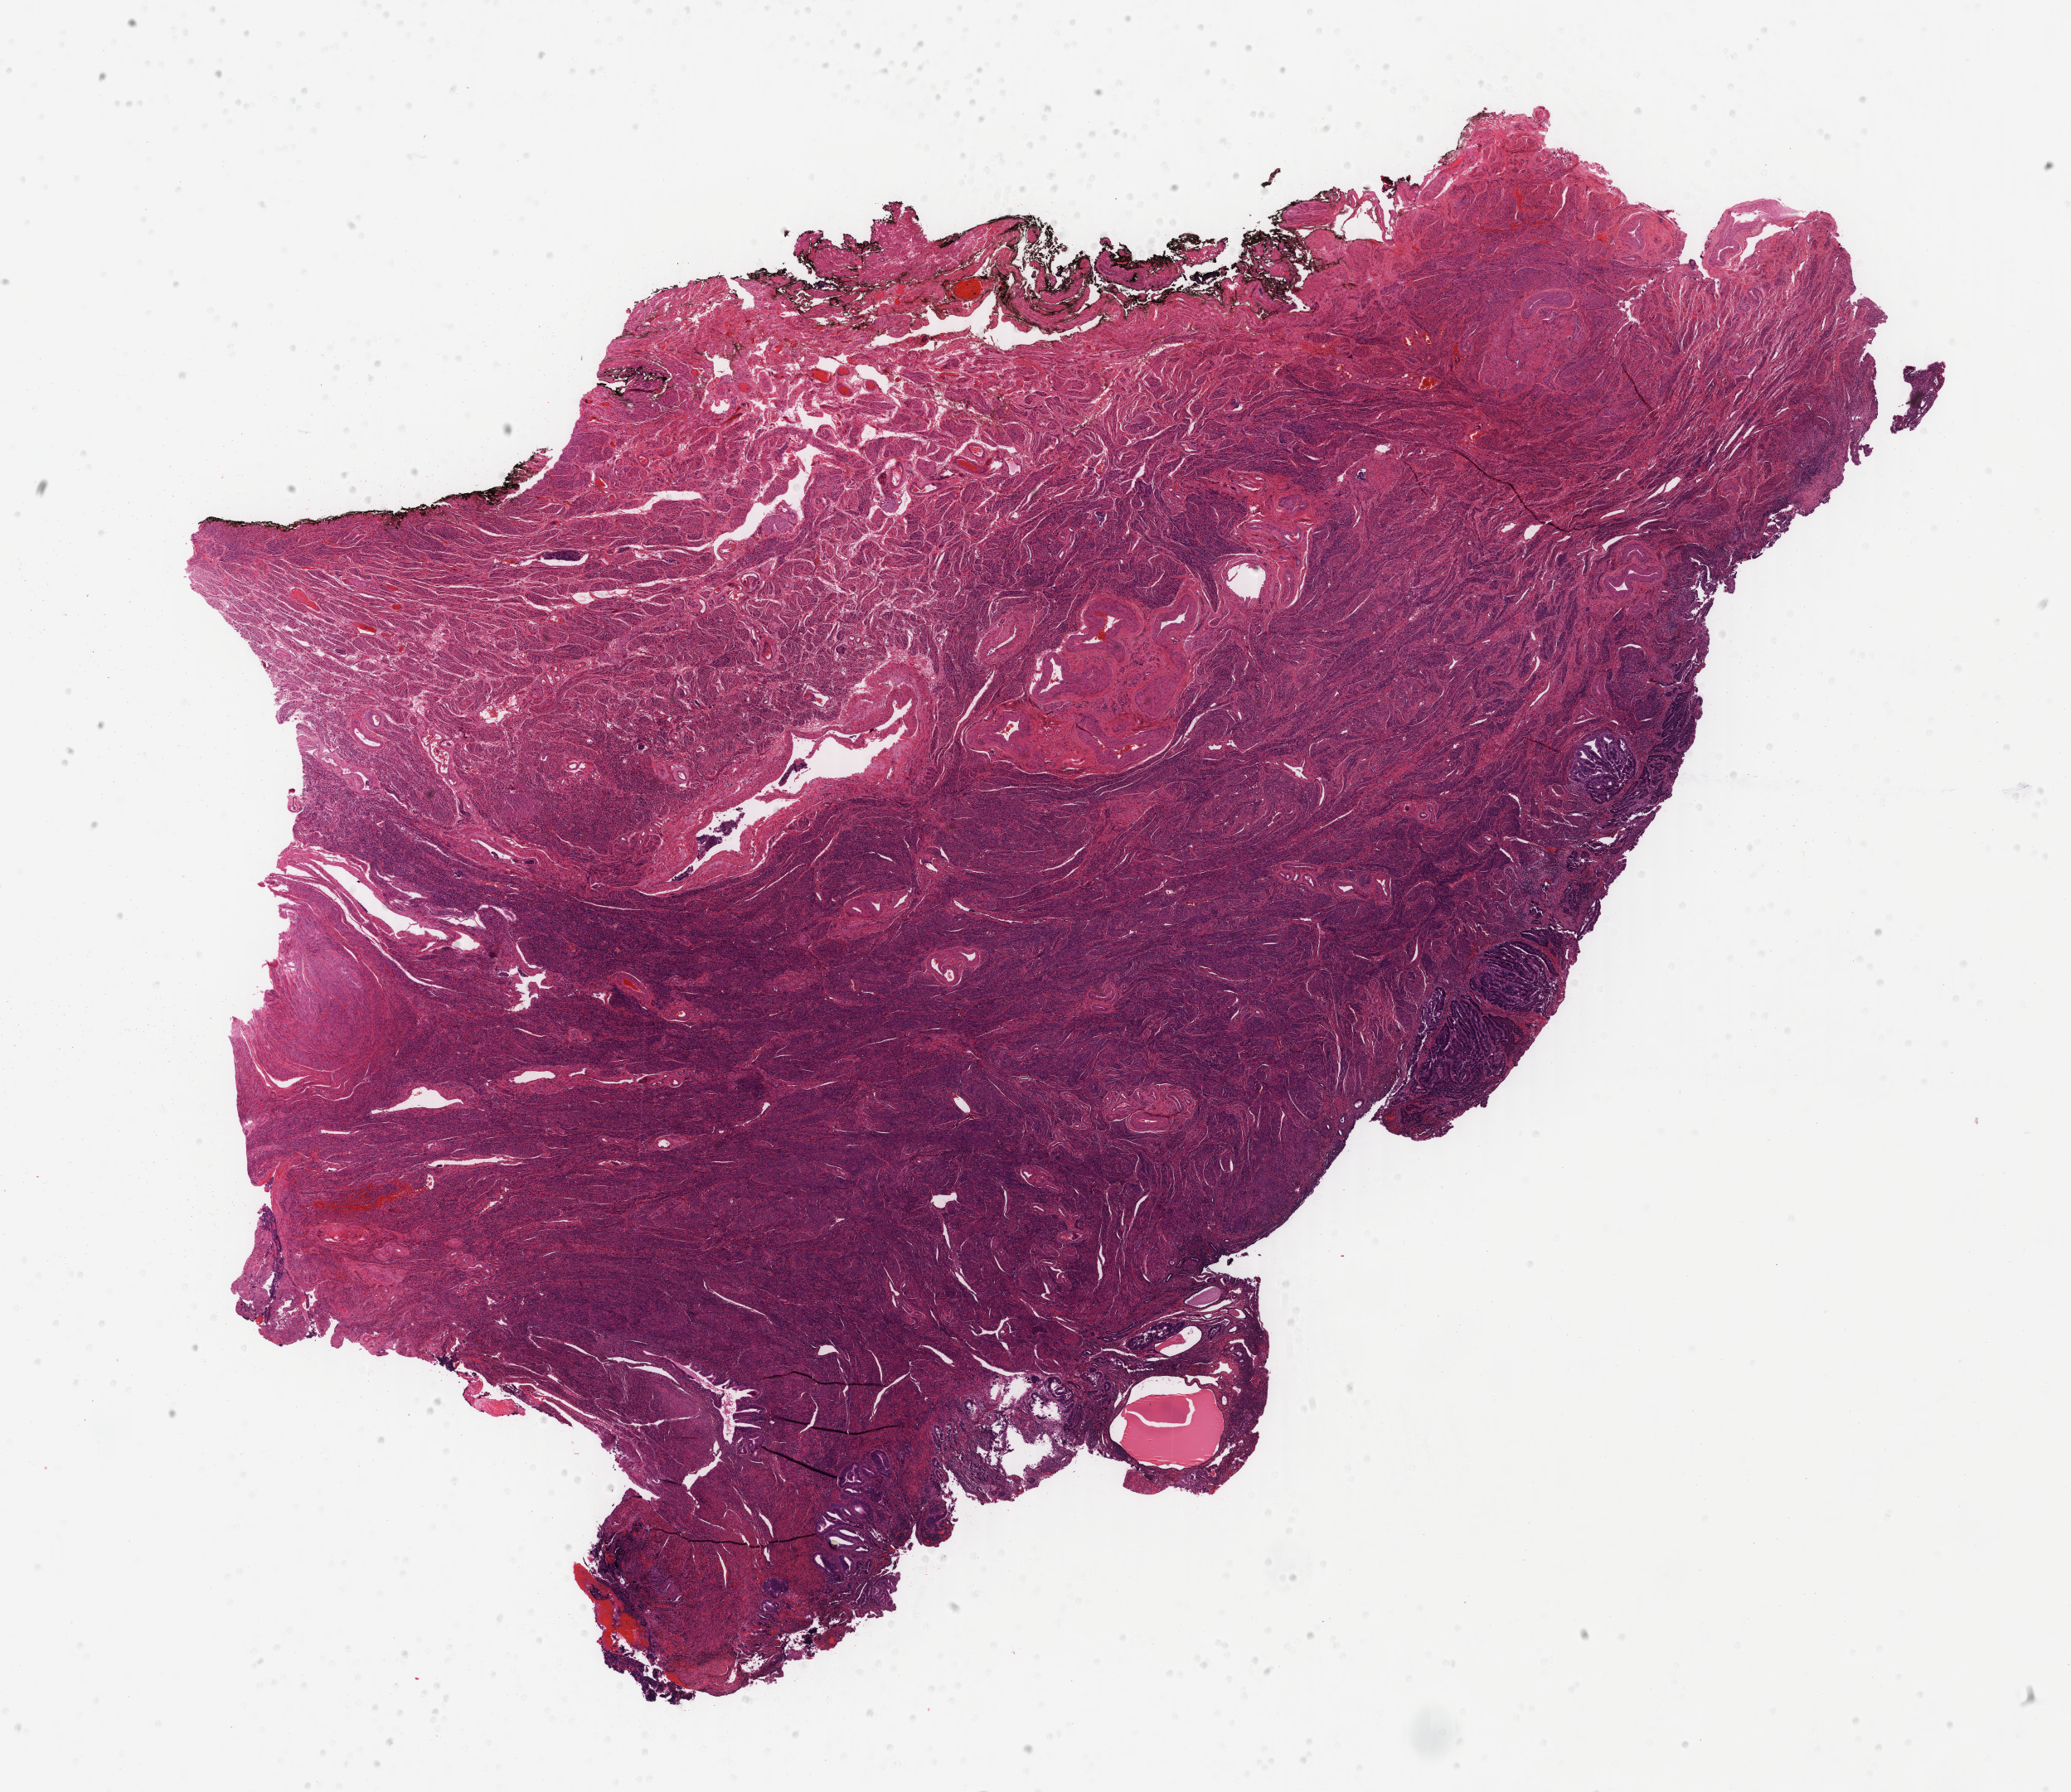
Whole-slide histology image, H&E — a low-resolution overview of the entire scanned area, about 19.8 x 17.2 mm. Formalin-fixed paraffin-embedded (FFPE) diagnostic section. Sample: primary tumour, uterus. Female patient; age at initial diagnosis 64 years. Histologic grade: G2 (moderately differentiated).
- FIGO stage: IB
- histologic diagnosis: Endometrioid adenocarcinoma, NOS